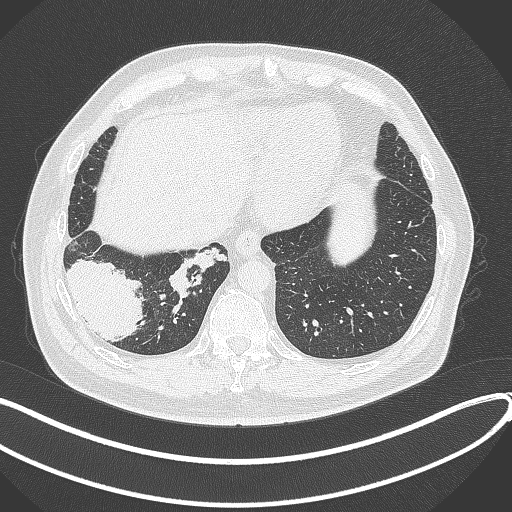
Chest CT, one axial slice. Position 77 of 360 along the scan axis. 120 kVp. Lung window (W 1500 / L -600 HU). 1 mm slice thickness. 512 × 512 image matrix, field of view 400 × 400 mm. Patient: male, 59 years.
Outlined on this slice (rectangle marked by the reading radiologist):
- lung tumour (recorded histology: adenocarcinoma): bounding box [x1, y1, x2, y2] px = [63, 256, 153, 341]